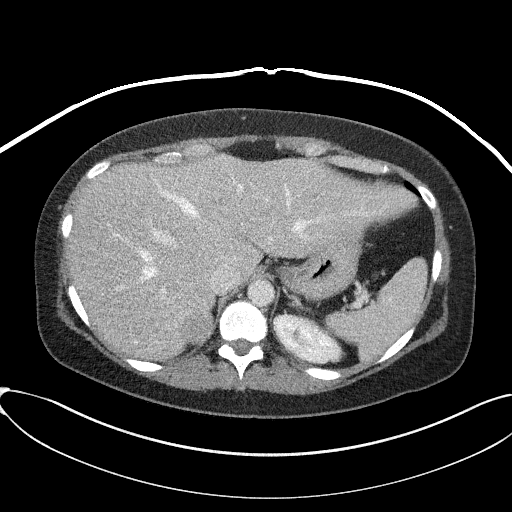
Contrast-enhanced abdominal CT, one axial slice; position 65 of 95 along the scan axis; reconstruction kernel I41f/2; intravenous contrast given; soft-tissue window (W 400 / L 40 HU); 512 × 512 image matrix. Female patient, age 46 years. Case-level facts recorded for this patient, not image findings: diagnosis: adrenocortical carcinoma; tumour side: right adrenal; tumour size at pathology: 7.2 cm; Ki-67 index: 50 %; stage (as recorded): 4.
Annotated regions visible in this slice (semi-automatic segmentation, software-assisted and operator-edited):
- mass: bounding box <182,310,213,342> (left, top, right, bottom; pixels)